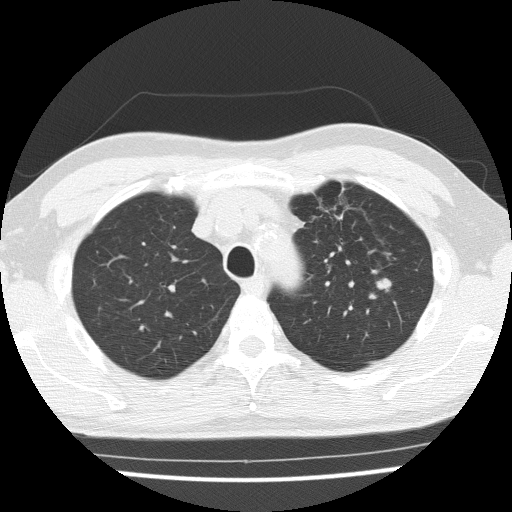
Low-dose screening chest CT, one axial slice; slice 116 of 154 in the series (ordered by position); 120 kVp; lung window (W 1500 / L -600 HU); 2 mm slice thickness; 512 × 512 image matrix.
Structures marked on this image (expert manual segmentation):
- lesion 1 (tumor, upper lobe of left lung): bounding box [x1, y1, x2, y2] px = [377, 278, 391, 291]